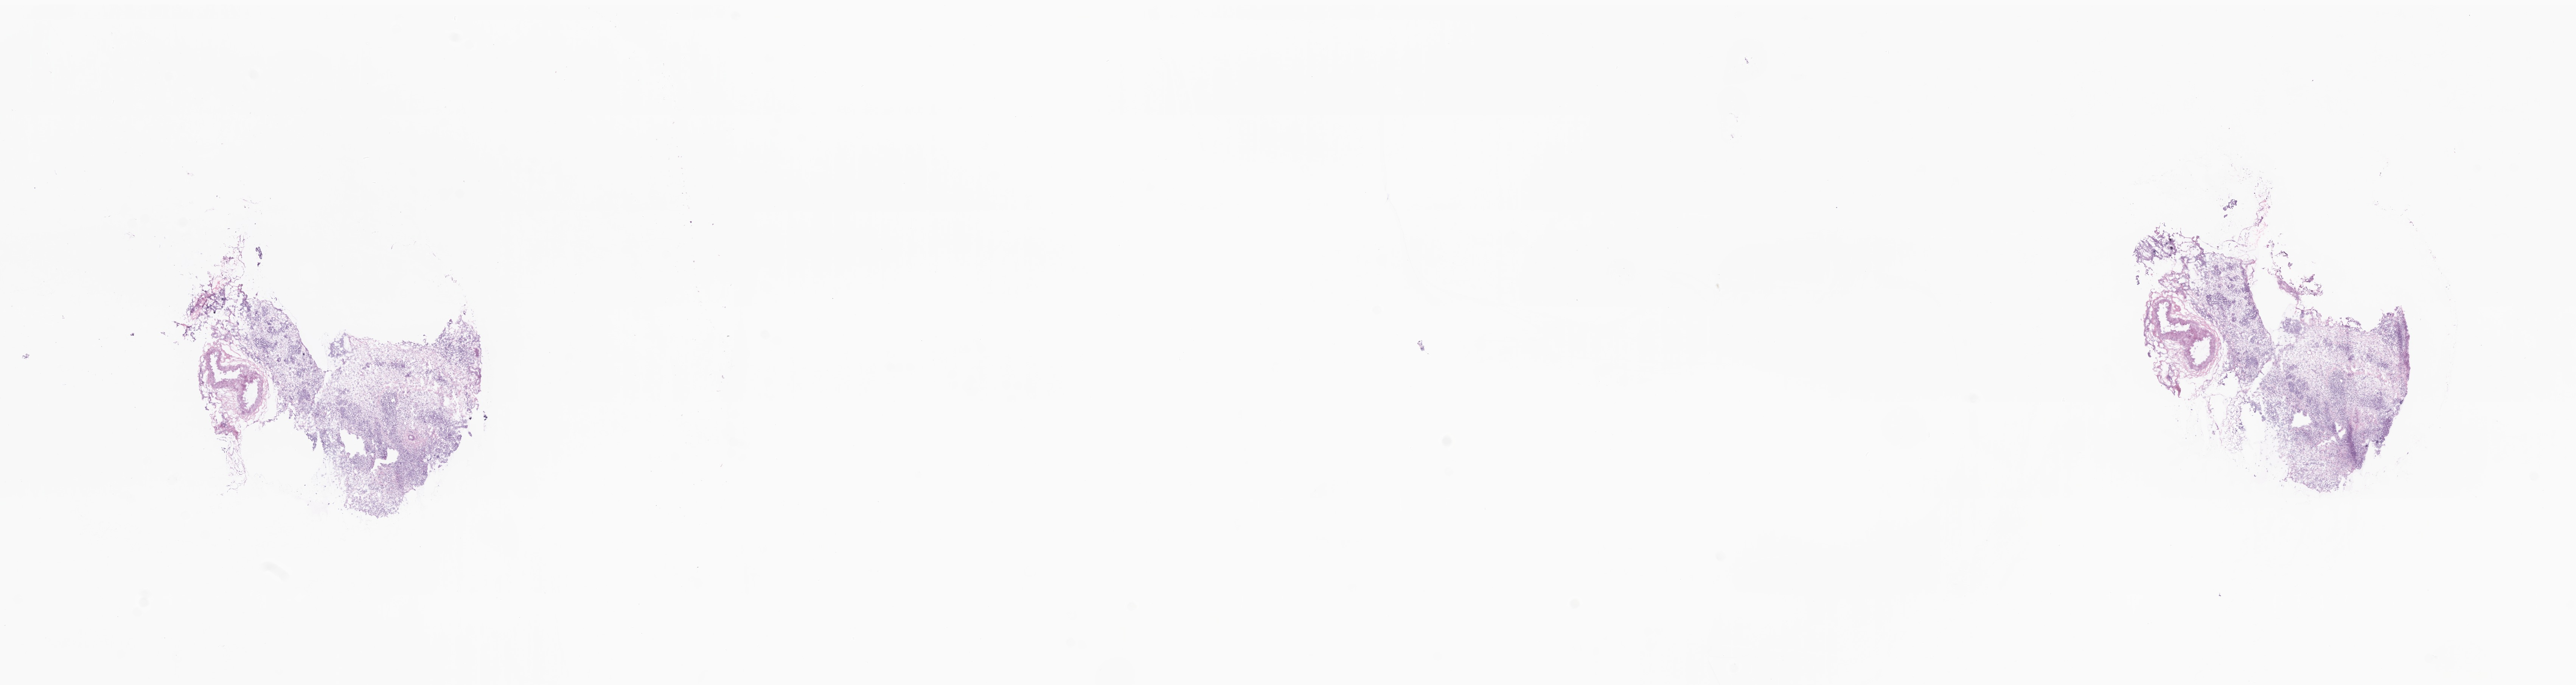
Whole-slide image, hematoxylin and eosin (H&E) stain, whole scanned area (about 28.7 x 7.6 mm) shown as a low-resolution overview, frozen section, specimen: metastatic tumor tissue, resected from specified parts of peritoneum. Patient: female, age at initial diagnosis 62 years. Slide review estimates, as recorded: tumor cells 40%, tumor nuclei 71%, stromal cells 38%, necrosis 10%, normal cells 12%. Infiltration values recorded for this section: lymphocyte infiltration 8%, monocyte infiltration 0%, neutrophil infiltration 0%.
Patient diagnosis (primary): High grade serous carcinoma.